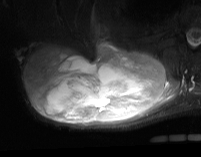
MRI of an extremity soft-tissue mass, one axial slice; slice 39 of 74 in the series (ordered by position); STIR; MR volume resampled by the dataset authors to the PET/CT grid (not the native acquisition matrix); 3.27 mm slice thickness; 201 × 157 image matrix, field of view 196 × 153 mm. Male patient. Case-level facts recorded for this patient, not image findings: histological type: pleiomorphic spindle cell undifferentiated; grade: high; site of the primary tumour: right parascapusular.
Outlined on this slice (expert contour drawn on MRI and transferred to this co-registered scan by the dataset authors):
- gross tumour volume including surrounding oedema: bounding box [x1, y1, x2, y2] px = [24, 39, 180, 126]
- gross tumour volume (mass): [24, 43, 166, 124]